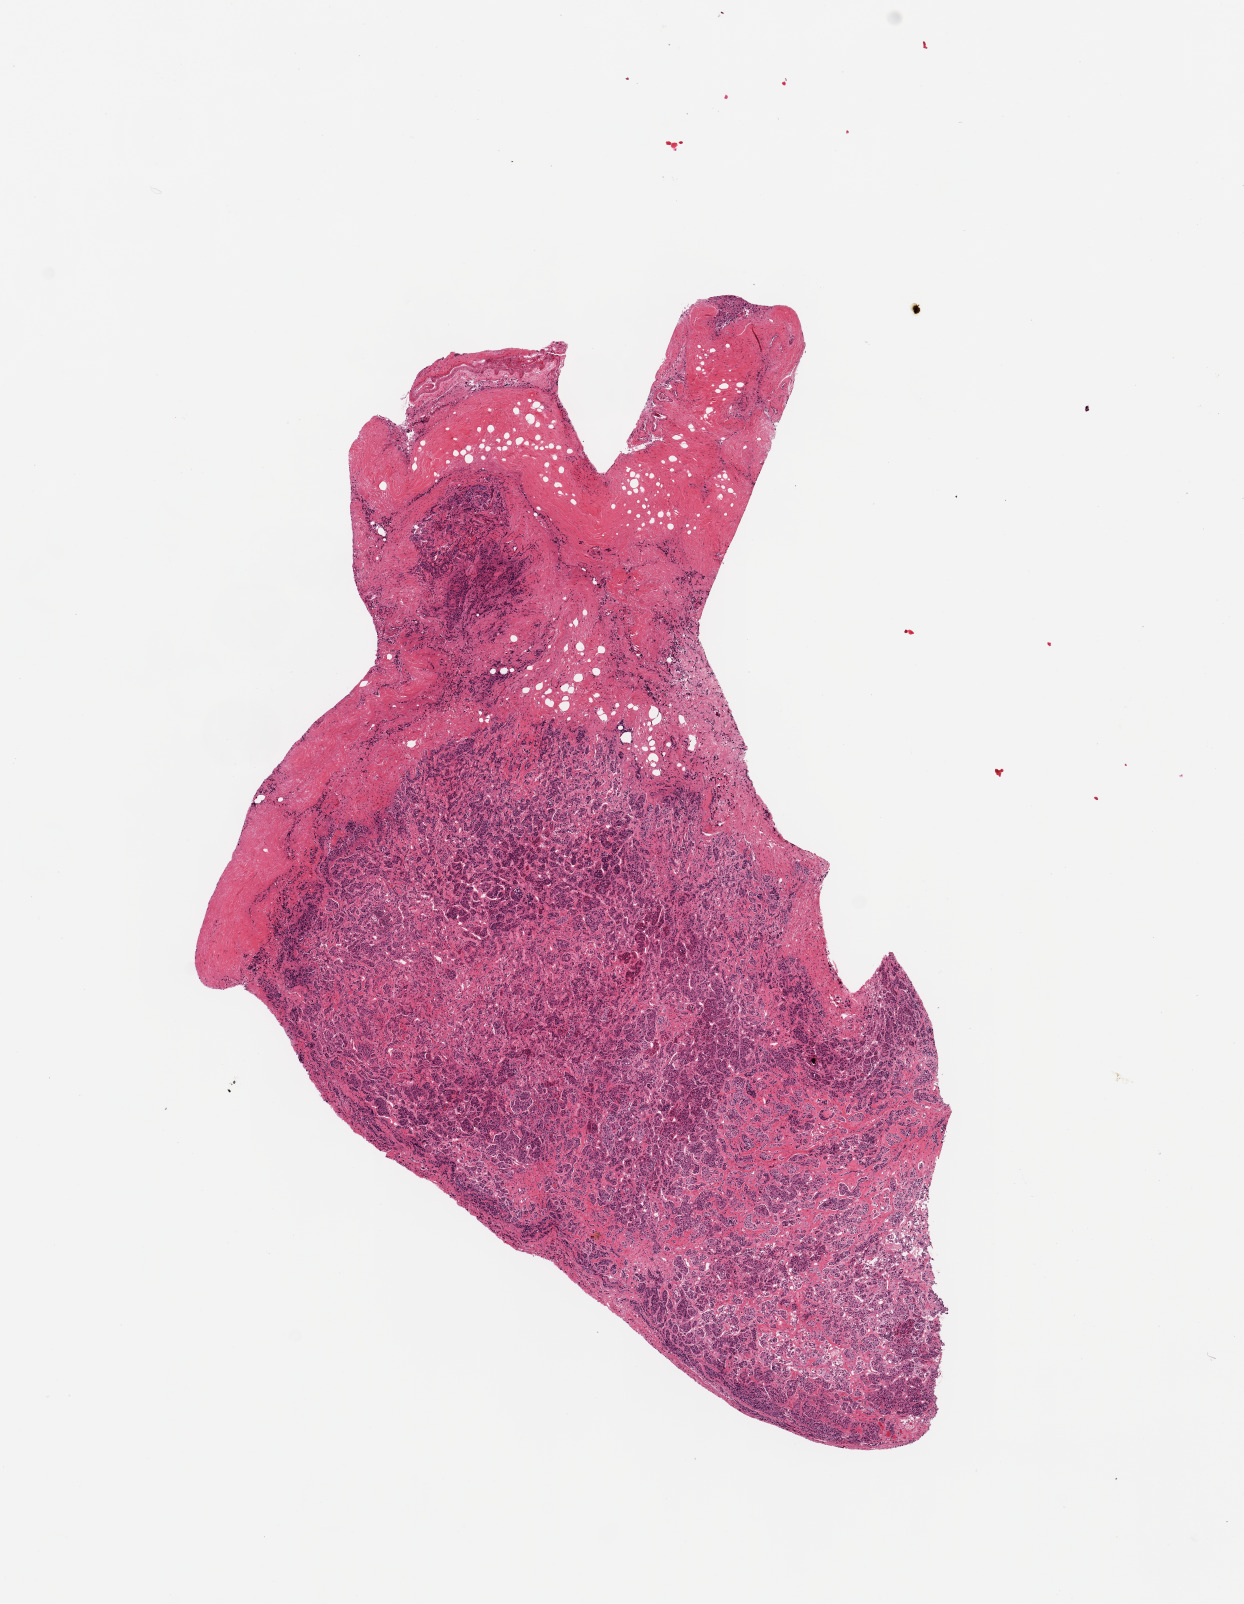
Hematoxylin and eosin (H&E) whole-slide image, low-resolution overview of the scanned area, about 9.8 x 12.7 mm (acquisition: 20x scan); PAXgene-fixed, paraffin-embedded tissue; sampled site (target tissue): pituitary; donor tissue sample. Male donor.
Review note (as recorded): 1 piece; thick capsule along edge.